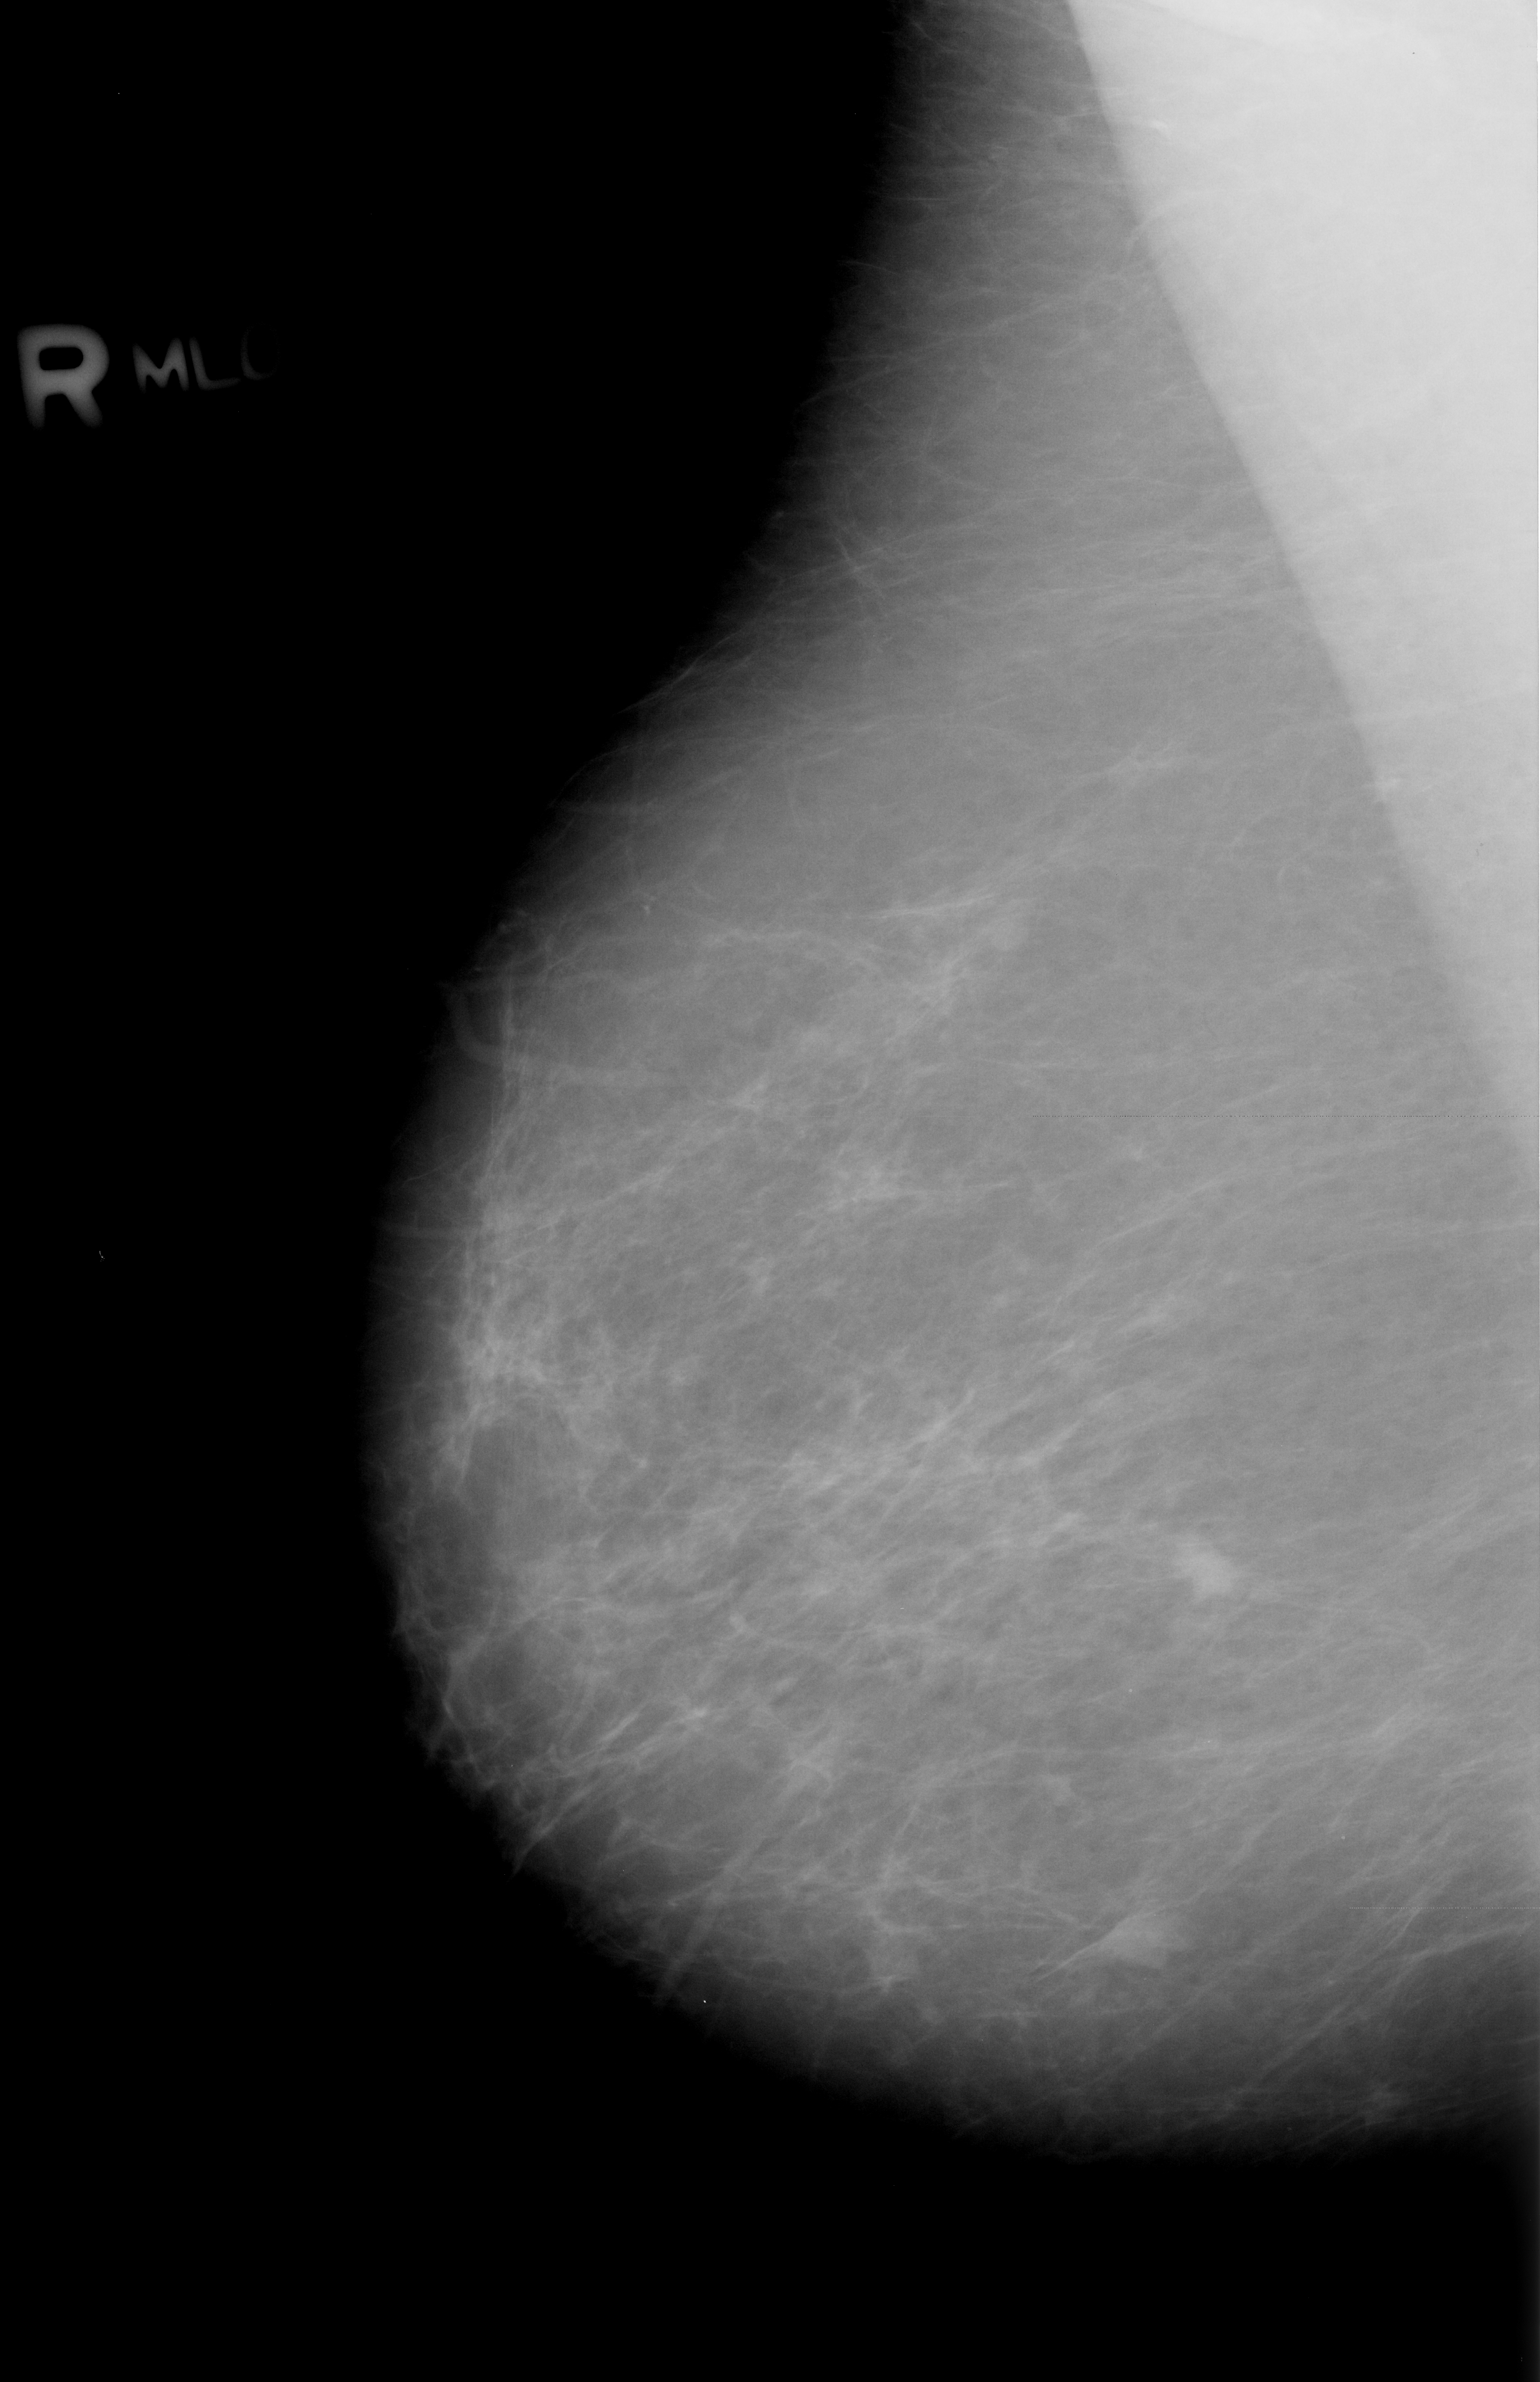
Mammogram (digitized film), right breast, MLO view.
Abnormality record for this image: Finding 1 of 2: mass, shape irregular, margins ill defined; BI-RADS assessment category 4; pathology (as recorded): malignant. Finding 2 of 2: mass, shape irregular, margins ill defined; BI-RADS assessment category 4; subtlety rating 3 on a 1 (subtle) to 5 (obvious) scale; pathology (as recorded): malignant.